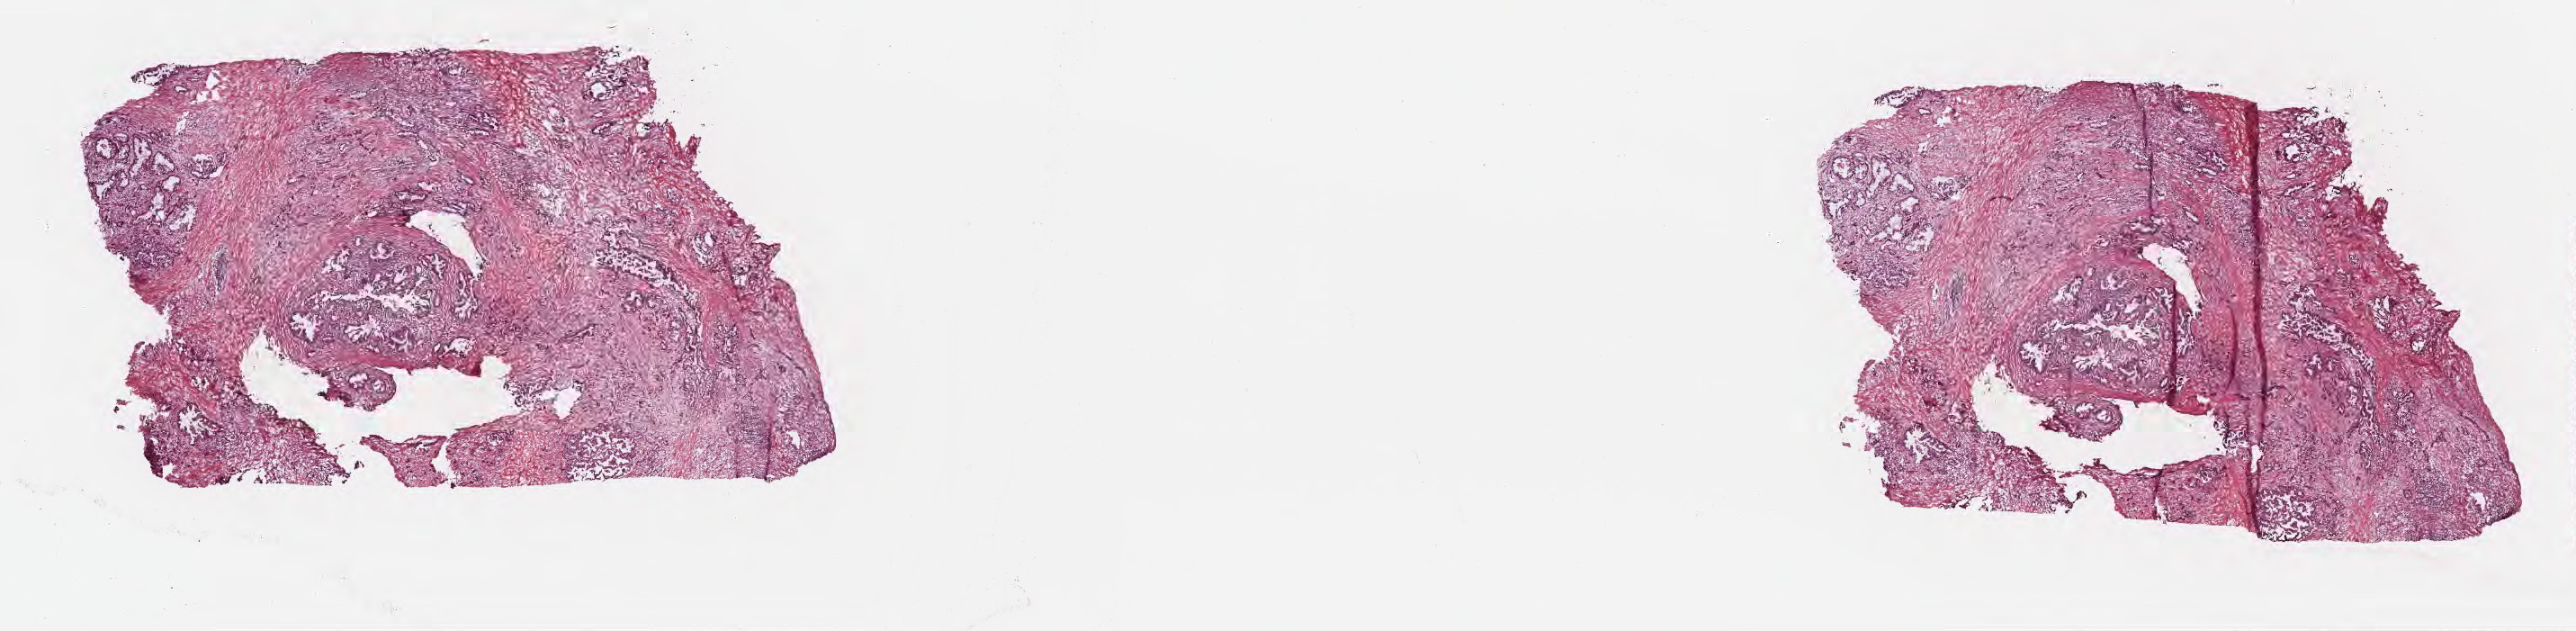
Hematoxylin and eosin (H&E) whole-slide image — whole scanned area (about 23.2 x 5.7 mm) shown as a low-resolution overview. Frozen section. Primary tumor. Site: tail of pancreas. Male, age 74 years at initial diagnosis. Tumor grade: G2 (moderately differentiated). Composition of this section per pathologist review: tumor cells 30%, tumor nuclei 40%, stromal cells 70%, necrosis 0%, normal cells 0%. Inflammatory infiltration, as recorded: lymphocyte infiltration 0%, monocyte infiltration 0%, neutrophil infiltration 0%.
Section: bottom of the tissue portion. AJCC pathologic stage: Stage IB. Diagnosis: Infiltrating duct carcinoma, NOS.